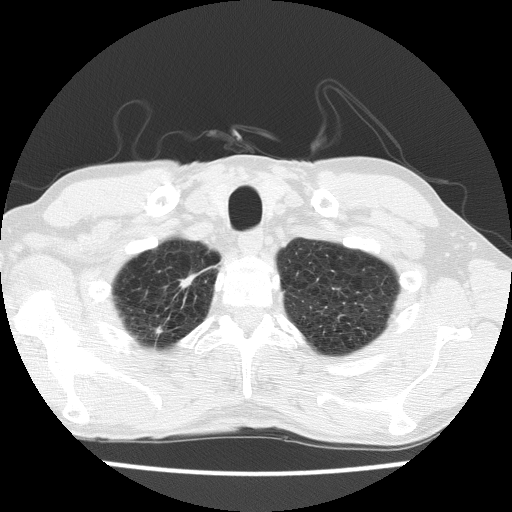
Chest CT (low-dose screening protocol), one axial image; second screening round (one year after baseline); lung window (W 1500 / L -600 HU); lung (sharp) reconstruction kernel (FC51); 512 × 512 image matrix. Male, age 63 years at enrolment. Current smoker at enrolment.
Expert-annotated lung lesion, box from (x=137, y=263) to (x=207, y=332) px. Screening reader's record for this exam: no non-calcified nodule ≥4 mm recorded. Official screen result: negative screen, minor abnormalities not suspicious for lung cancer.